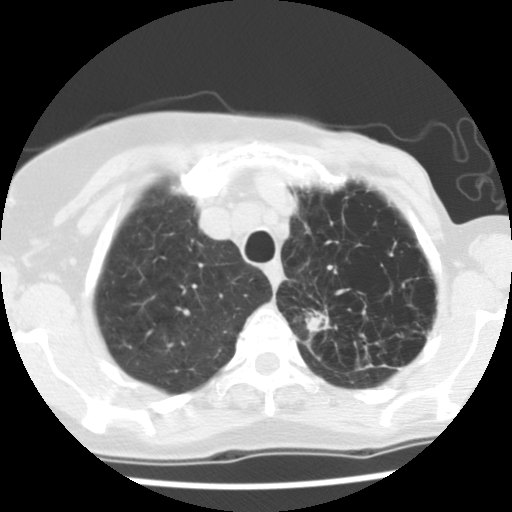
Axial slice from a low-dose chest CT screening exam. Baseline annual screen. Lung window (W 1500 / L -600 HU). Standard (soft-tissue) reconstruction kernel (STANDARD). Slice 24 of 128 in the series. 512 × 512 image matrix, field of view 290 × 290 mm. Female participant, aged 67 years at enrolment. Current smoker at enrolment.
• Expert reader's lesion annotation, bounding box <289,298,389,381> (left, top, right, bottom; pixels).
• The screening reader recorded 2 non-calcified nodules or masses ≥4 mm on this exam (left upper lobe, left lower lobe); which of them this box marks is not recorded.
• Lung cancer was diagnosed 109 days after this screen: adenocarcinoma, NOS, left upper lobe, poorly differentiated (G3), stage IIB (AJCC 6th edition), 45 mm at pathology.